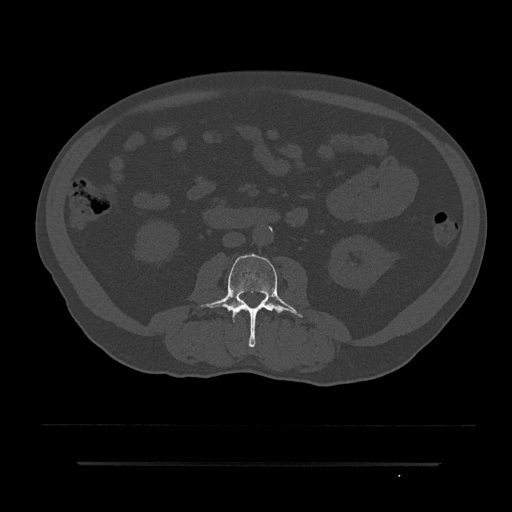
CT including the spine, one axial slice. Position 9 of 797 along the scan axis. 120 kVp. Bone window (W 1800 / L 400 HU). 512 × 512 image matrix. Patient: male, 59 years. From the clinical record (not read from this slice): primary cancer: bile ducts; vertebrae with lytic lesions (as recorded): T10.
Annotated regions visible in this slice (semi-automatically segmented with operator editing):
- L2 vertebra: box from (x=240, y=309) to (x=249, y=317) px
- L3 vertebra: (x=199, y=254)–(x=304, y=347)